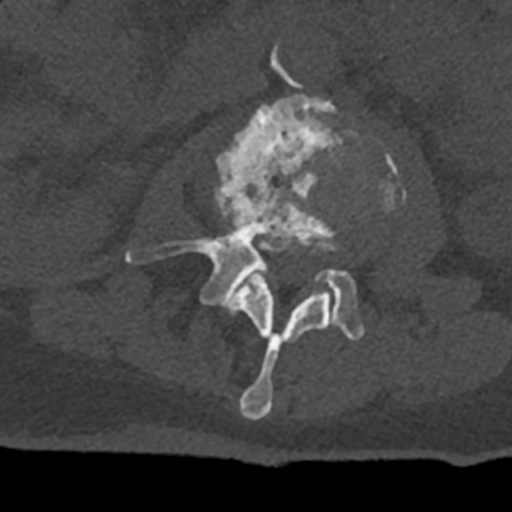
CT including the spine, one axial slice; reconstruction kernel Br40s/3; bone window (W 1800 / L 400 HU); 0.5 mm slice thickness; 512 × 512 image matrix, field of view 160 × 160 mm. Patient: male, 74 years. From the clinical record (not read from this slice): primary cancer: renal.
Annotated regions visible in this slice (semi-automatically segmented with operator editing):
- L2 vertebra: bounding box [x1, y1, x2, y2] px = [229, 194, 331, 420]
- L3 vertebra: [125, 94, 394, 341]